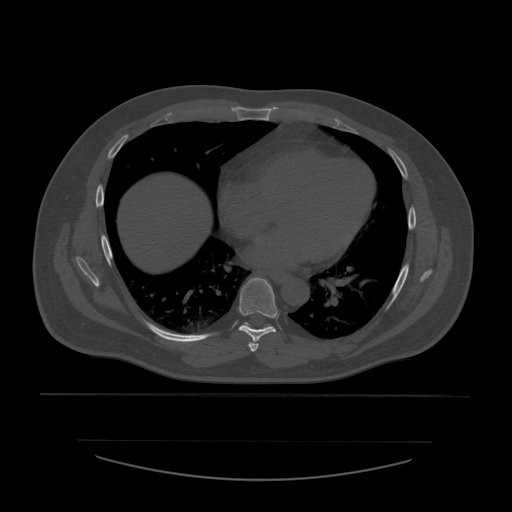
CT including the spine, one axial slice. 120 kVp. Bone window (W 1800 / L 400 HU). 1.25 mm slice thickness. 512 × 512 image matrix, field of view 441 × 441 mm. Patient age 44 years. From the clinical record (not read from this slice): primary cancer: soft tissue sarcoma.
Outlined on this slice (semi-automatically segmented with operator editing):
- T6 vertebra: bounding box [x1, y1, x2, y2] px = [248, 342, 259, 353]
- T7 vertebra: [239, 278, 279, 344]
- T8 vertebra: [246, 323, 270, 327]